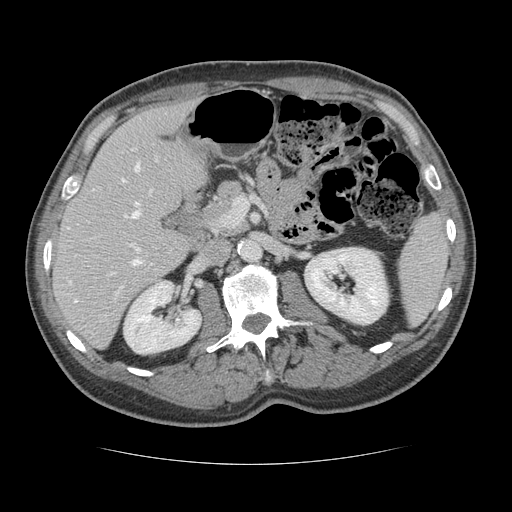
Contrast-enhanced abdominal CT, one axial slice. Position 68 of 134 along the scan axis. Reconstruction kernel STANDARD. Soft-tissue window (W 400 / L 40 HU). 512 × 512 image matrix. Male patient, age 68 years. From the clinical record (not read from this slice): diagnosis: colorectal cancer liver metastases, imaged before liver resection.
Outlined on this slice (expert manual segmentation):
- hepatic veins: box from (x=69, y=163) to (x=152, y=302) px
- liver: (x=53, y=103)–(x=209, y=347)
- planned liver remnant (the part of the liver to remain after resection): (x=53, y=103)–(x=209, y=336)
- portal vein (with intrahepatic branches): (x=111, y=215)–(x=142, y=274)